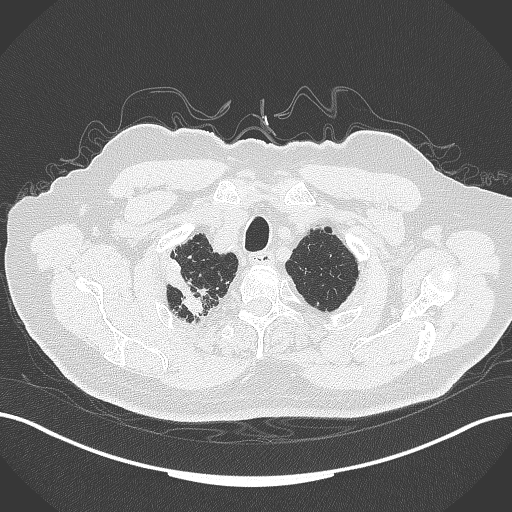
Chest CT, one axial slice. Position 326 of 389 along the scan axis. Reconstruction kernel B70f. 120 kVp. Lung window (W 1500 / L -600 HU). 512 × 512 image matrix, field of view 400 × 400 mm. Male patient, age 72 years. From the clinical record (not read from this slice): clinical TNM (as recorded): T1a N0 M0.
Outlined on this slice (bounding box drawn by a radiologist):
- lung tumour (recorded histology: squamous cell carcinoma): box from (x=164, y=251) to (x=208, y=314) px